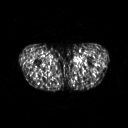
FDG PET of an extremity soft-tissue mass (from a PET/CT study), one axial slice. Slice 258 of 311 in the series (ordered by position). 128 × 128 image matrix. Male patient, age 29 years. Case-level facts recorded for this patient, not image findings: histological type: mixoid liposarcoma; grade: low; site of the primary tumour: left thigh.
Structures marked on this image (expert contour drawn on MRI and transferred to this co-registered scan by the dataset authors):
- gross tumour volume (mass): bounding box [x1, y1, x2, y2] px = [72, 56, 82, 65]